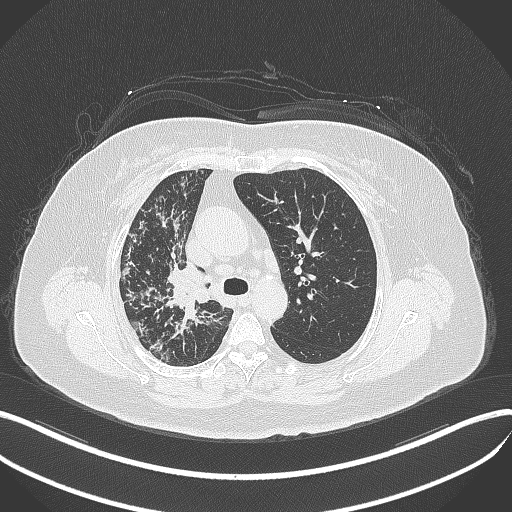
Chest CT, one axial slice. Slice 245 of 376 in the series (ordered by position). 120 kVp. Lung window (W 1500 / L -600 HU). 512 × 512 image matrix, field of view 400 × 400 mm. Female patient, age 60 years. Case-level facts recorded for this patient, not image findings: clinical TNM (as recorded): T1c N0 M0; histopathological grade: G1-G2.
Outlined on this slice (bounding box drawn by a radiologist):
- lung tumour (recorded histology: squamous cell carcinoma): bounding box [x1, y1, x2, y2] px = [167, 266, 213, 307]